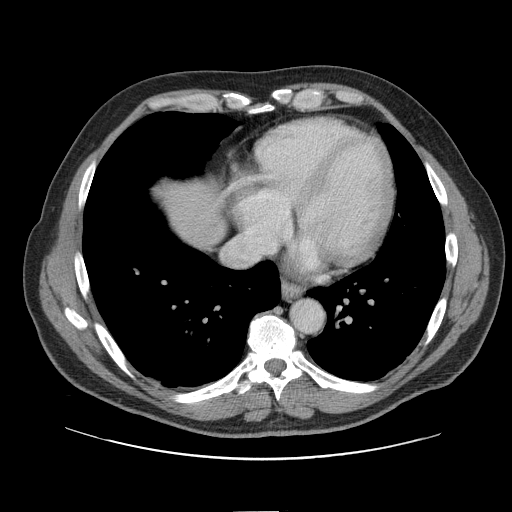
Contrast-enhanced abdominal CT, one axial slice; position 143 of 161 along the scan axis; 120 kVp; soft-tissue window (W 400 / L 40 HU); 2.5 mm slice thickness; 512 × 512 image matrix, field of view 412 × 412 mm. Male patient, age 66 years. Case-level facts recorded for this patient, not image findings: diagnosis: colorectal cancer liver metastases, imaged before liver resection.
Outlined on this slice (expert manual segmentation):
- liver: box from (x=165, y=182) to (x=224, y=246) px
- planned liver remnant (the part of the liver to remain after resection): (x=165, y=183)–(x=224, y=246)